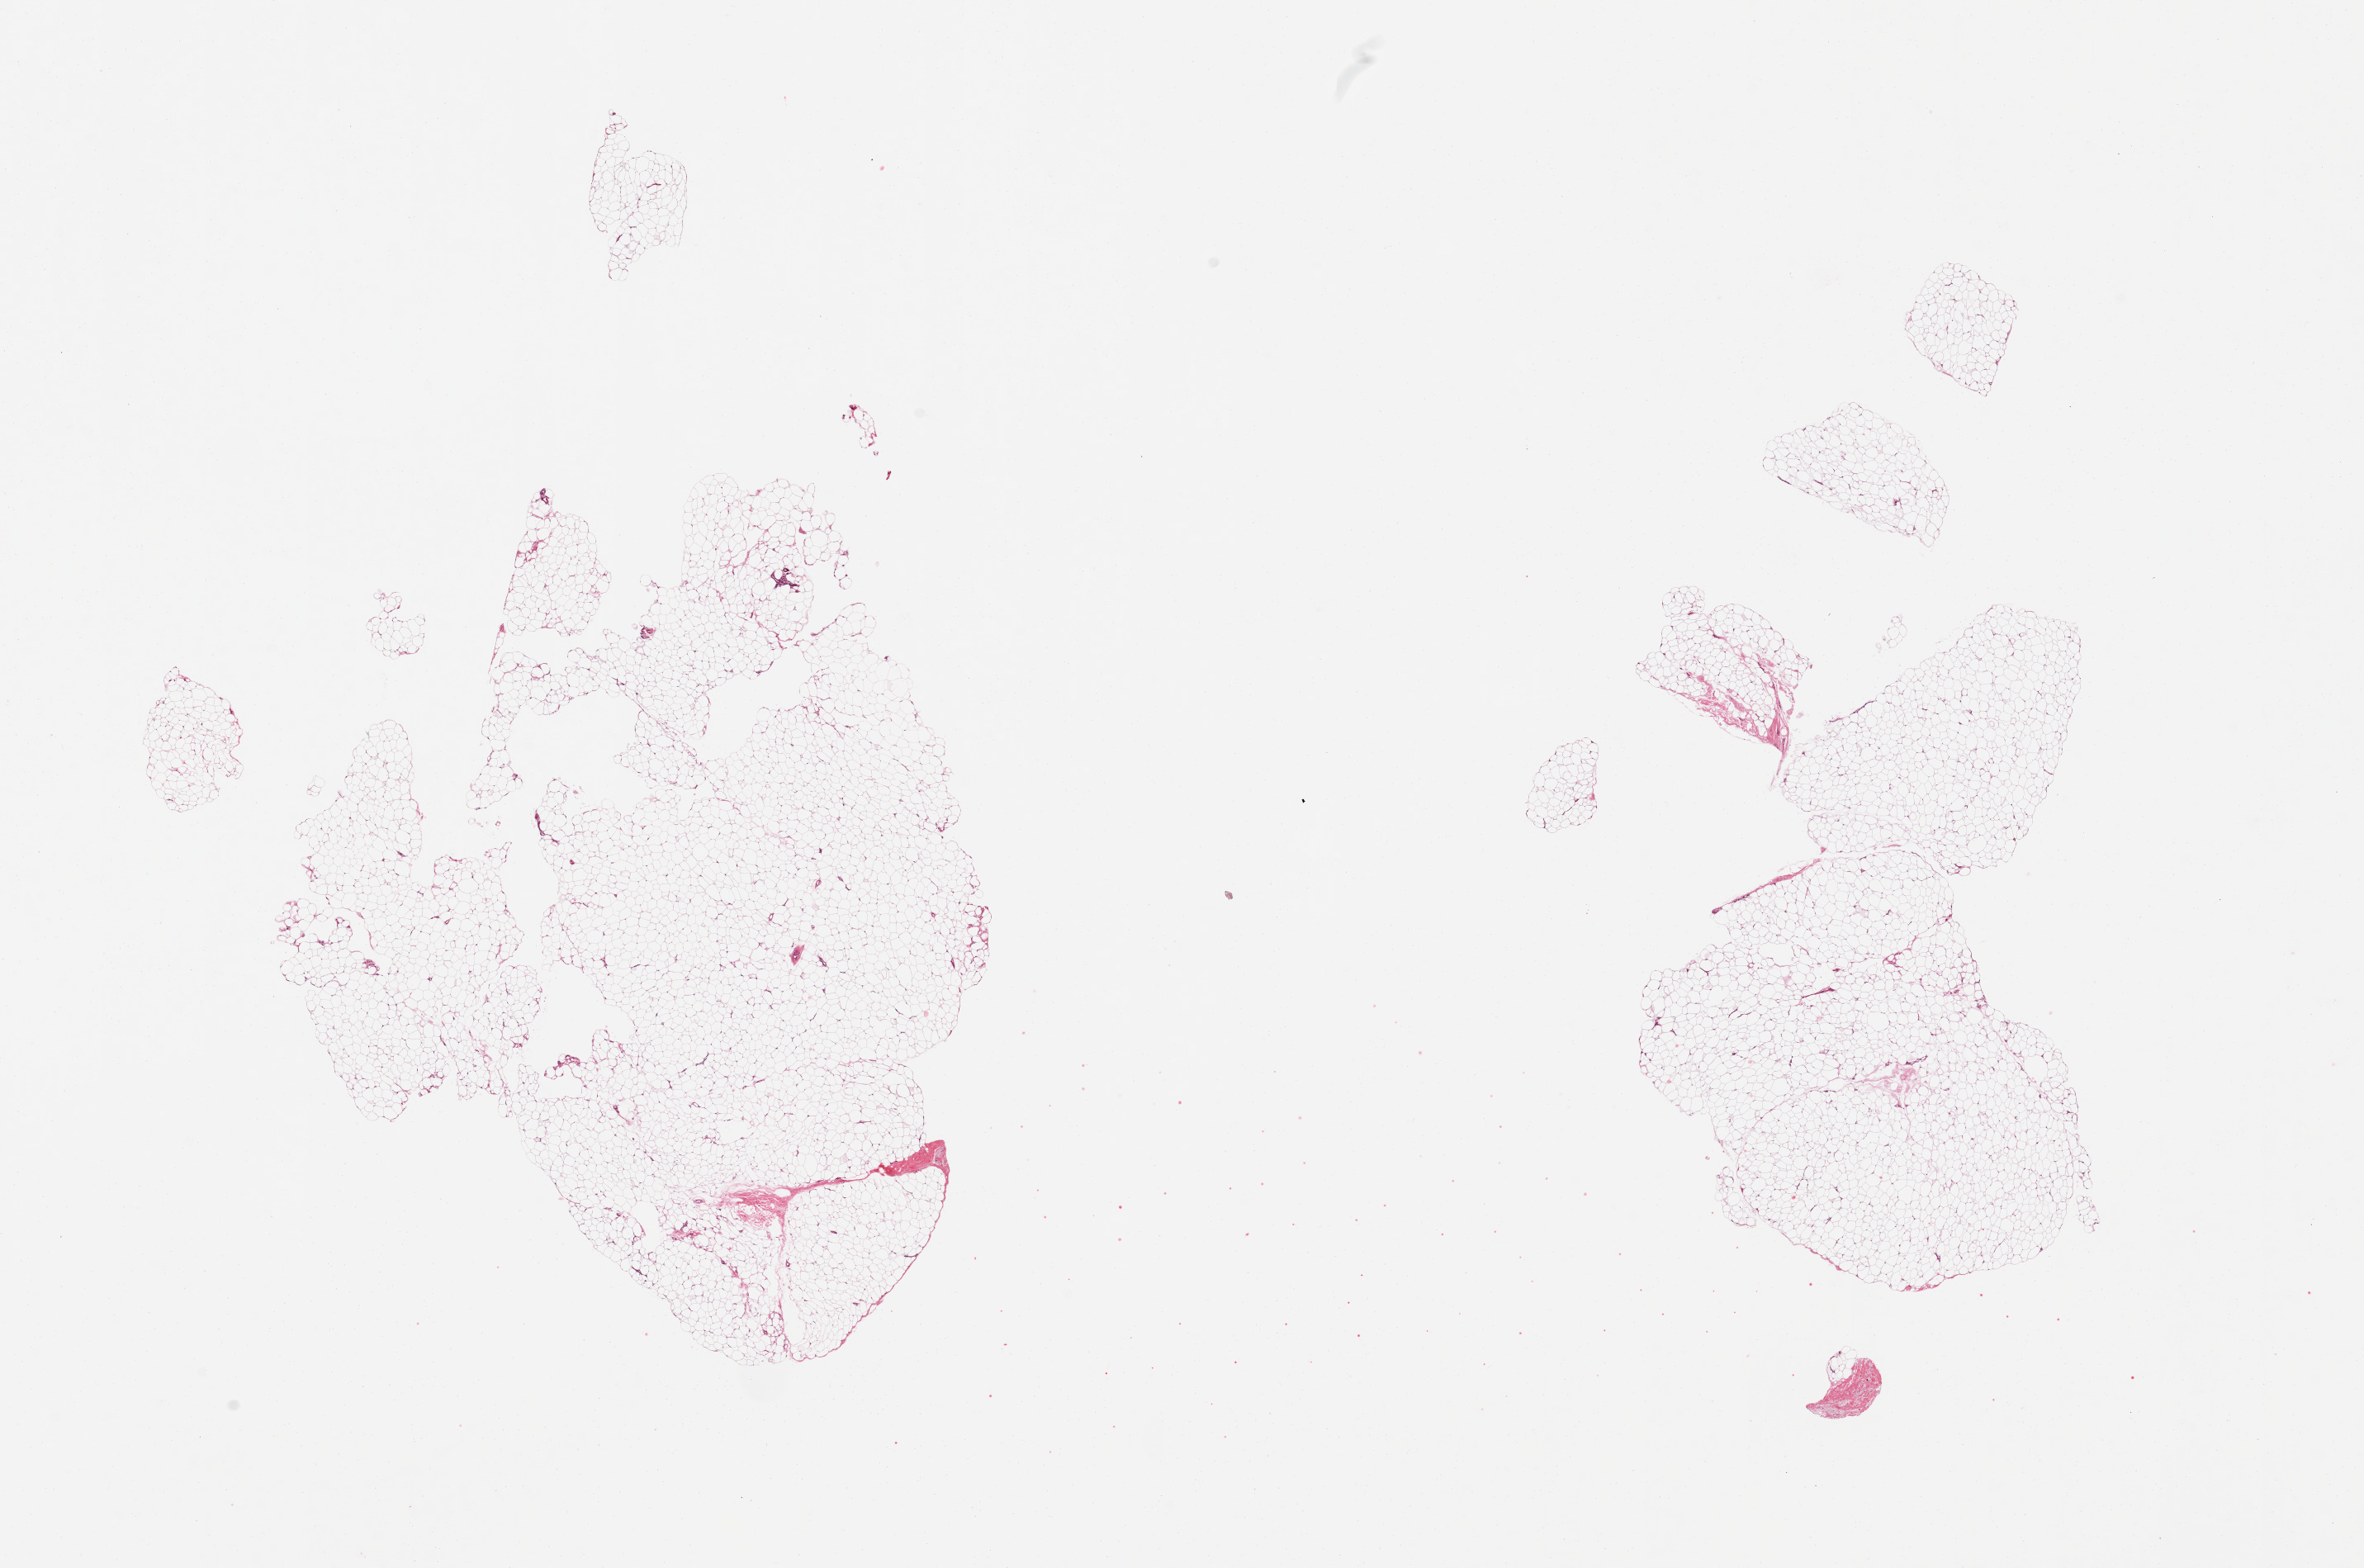
Whole-slide image, hematoxylin and eosin (H&E) stain, shown as a low-resolution overview of the whole scanned area (about 22.6 x 15.0 mm); PAXgene-fixed, paraffin-embedded tissue; target tissue: adipose tissue; donor tissue sample. Donor: female.
• reviewer comment on this tissue sample: 2 pieces, minimal fibrous/fascial tissue